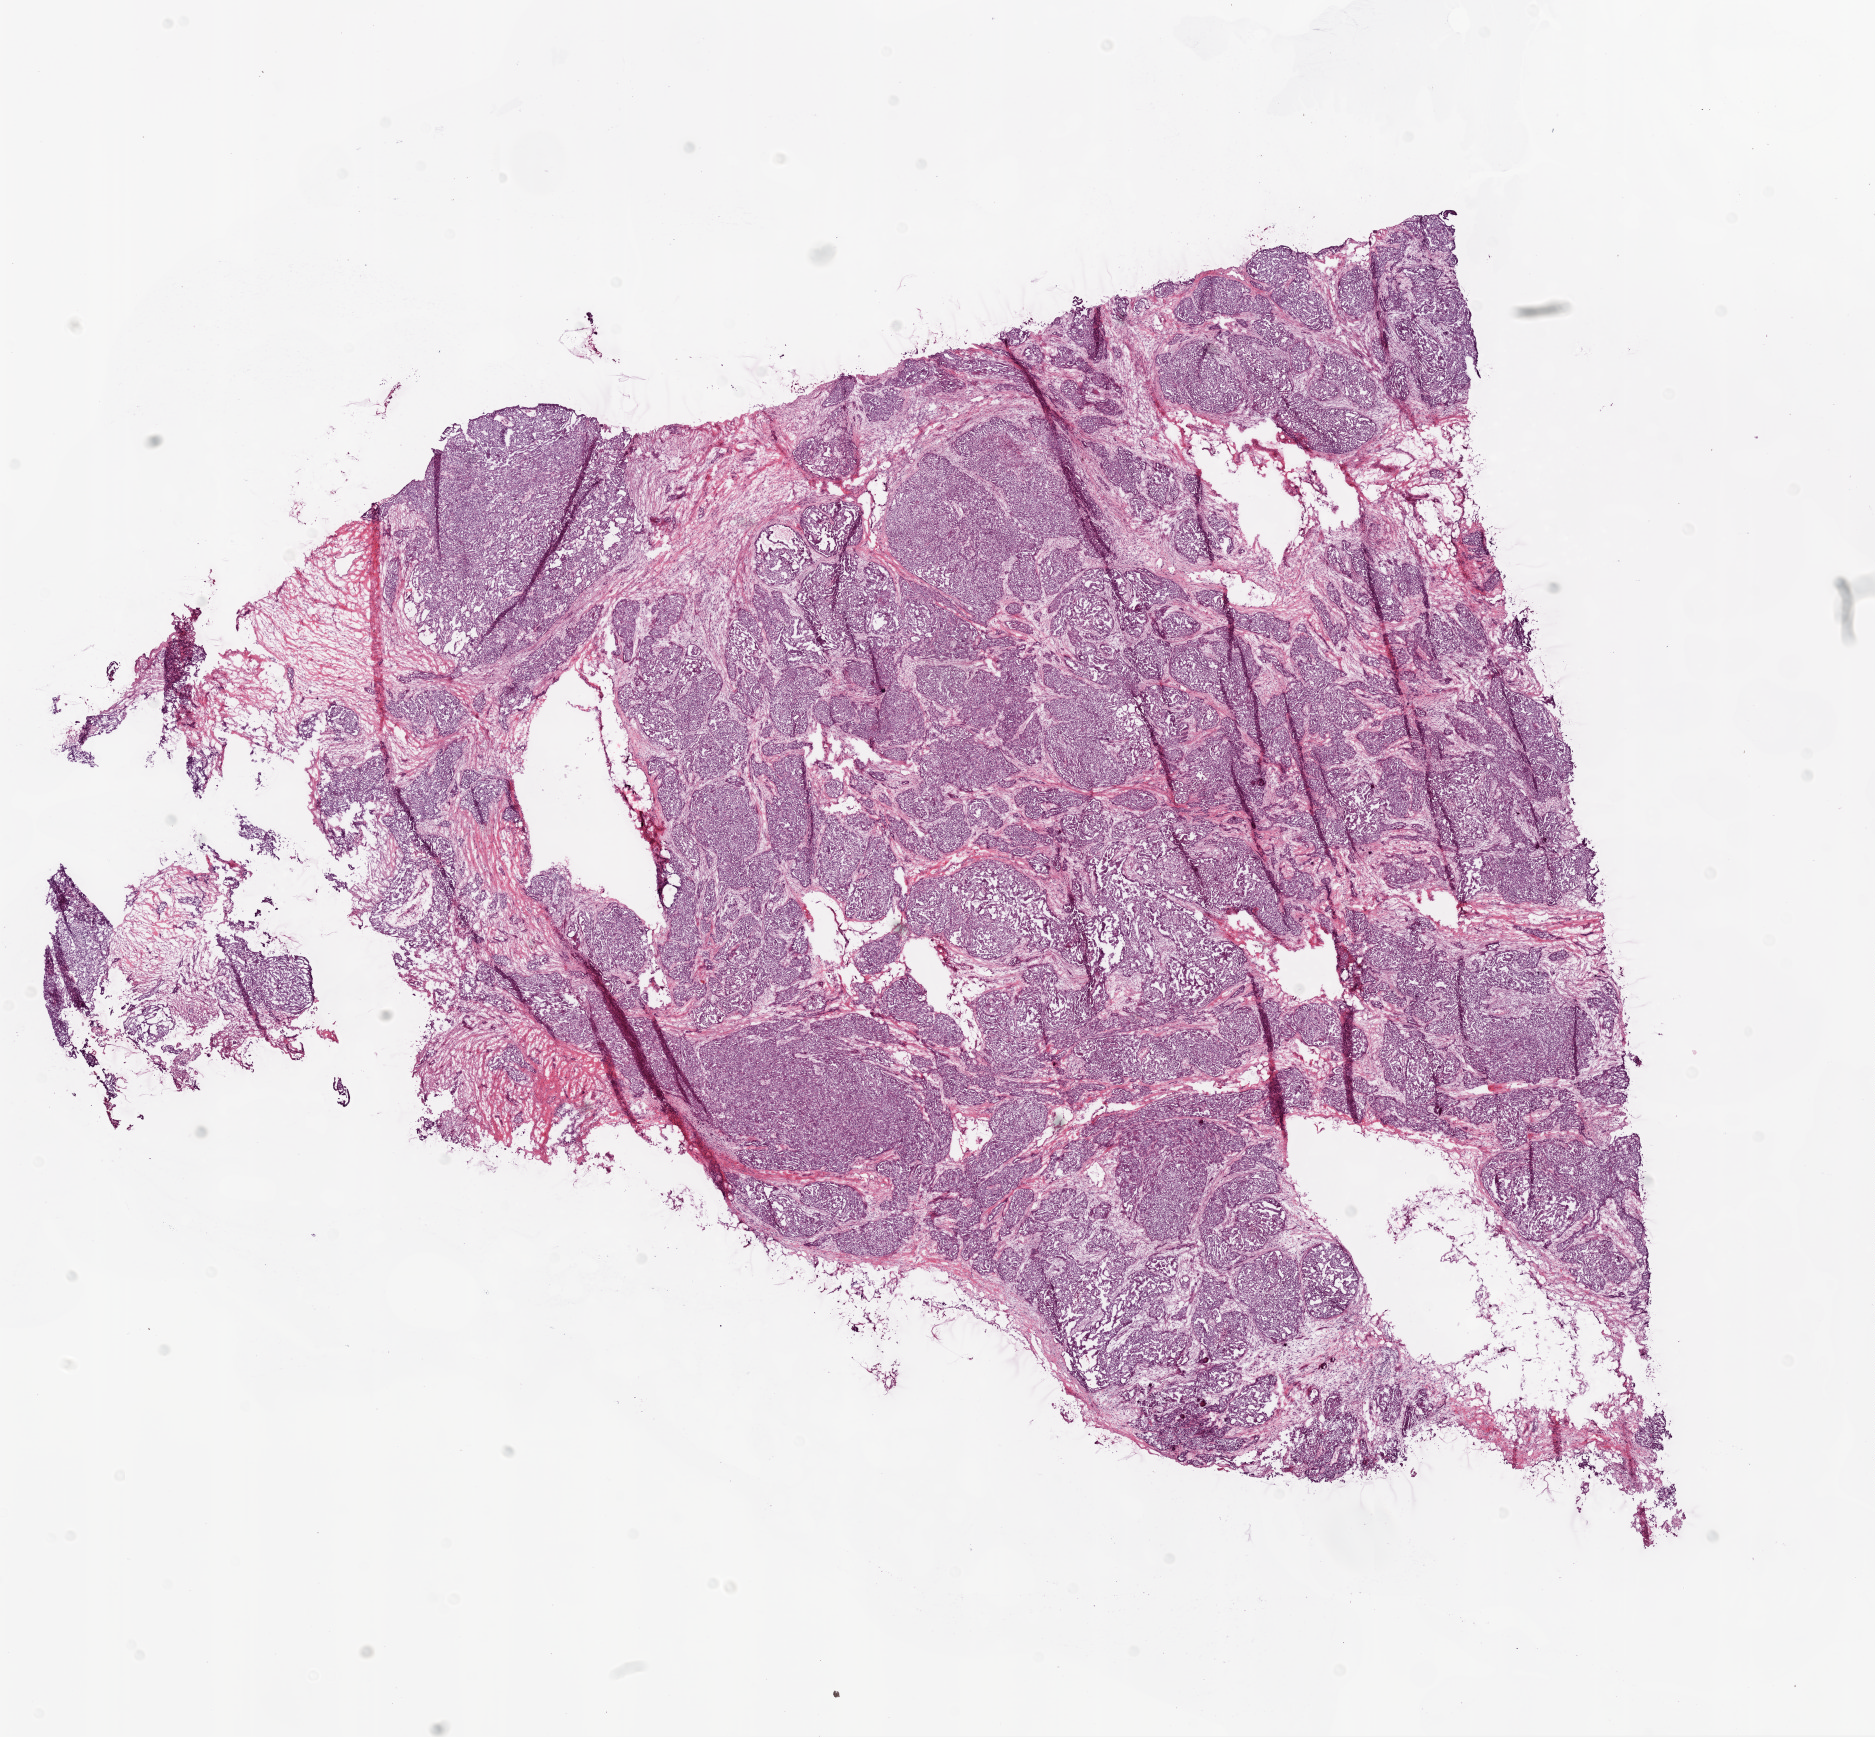
Hematoxylin and eosin (H&E) stained whole-slide image — low-resolution overview of the scanned area, about 15.0 x 13.9 mm (from a 20x scan); frozen section from the bottom of the tissue portion; primary tumour sample from the ovary. Female patient; age at initial diagnosis 63 years. Histologic grade: G3 (poorly differentiated). Composition of this section per pathologist review: tumour cells 85%, tumour nuclei 90%, normal cells 0%, stromal cells 15%, necrosis 0%. Inflammatory infiltration, as recorded: lymphocyte infiltration 5%.
Diagnosis: Serous cystadenocarcinoma, NOS. FIGO stage: IIIC.